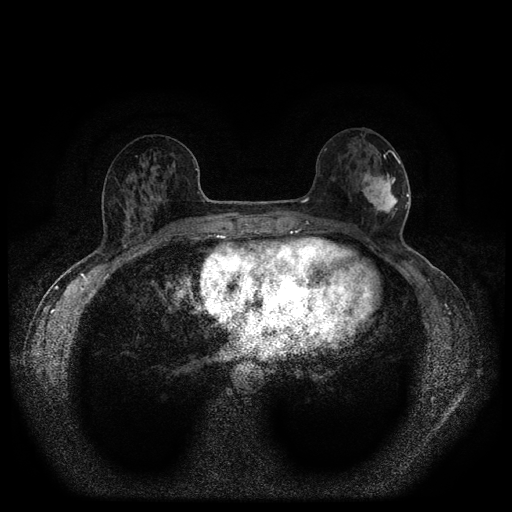
Breast MRI (dynamic contrast-enhanced, multi-phase), one axial slice; position 45 of 116 along the scan axis; dynamic contrast-enhanced series, time point 2 of 5 at this slice position (early post-contrast); 1.5 T; TE 2.7 ms, TR 5.4 ms; 2 mm slice thickness; 512 × 512 image matrix, field of view 330 × 330 mm. Patient: female, 56 years.
Outlined on this slice (semi-automatic segmentation, software-assisted and operator-edited):
- breast lesion (labelled 'tumour' in the annotation; benign lesions carry a separate 'benign' label): bounding box [x1, y1, x2, y2] px = [359, 169, 404, 215]